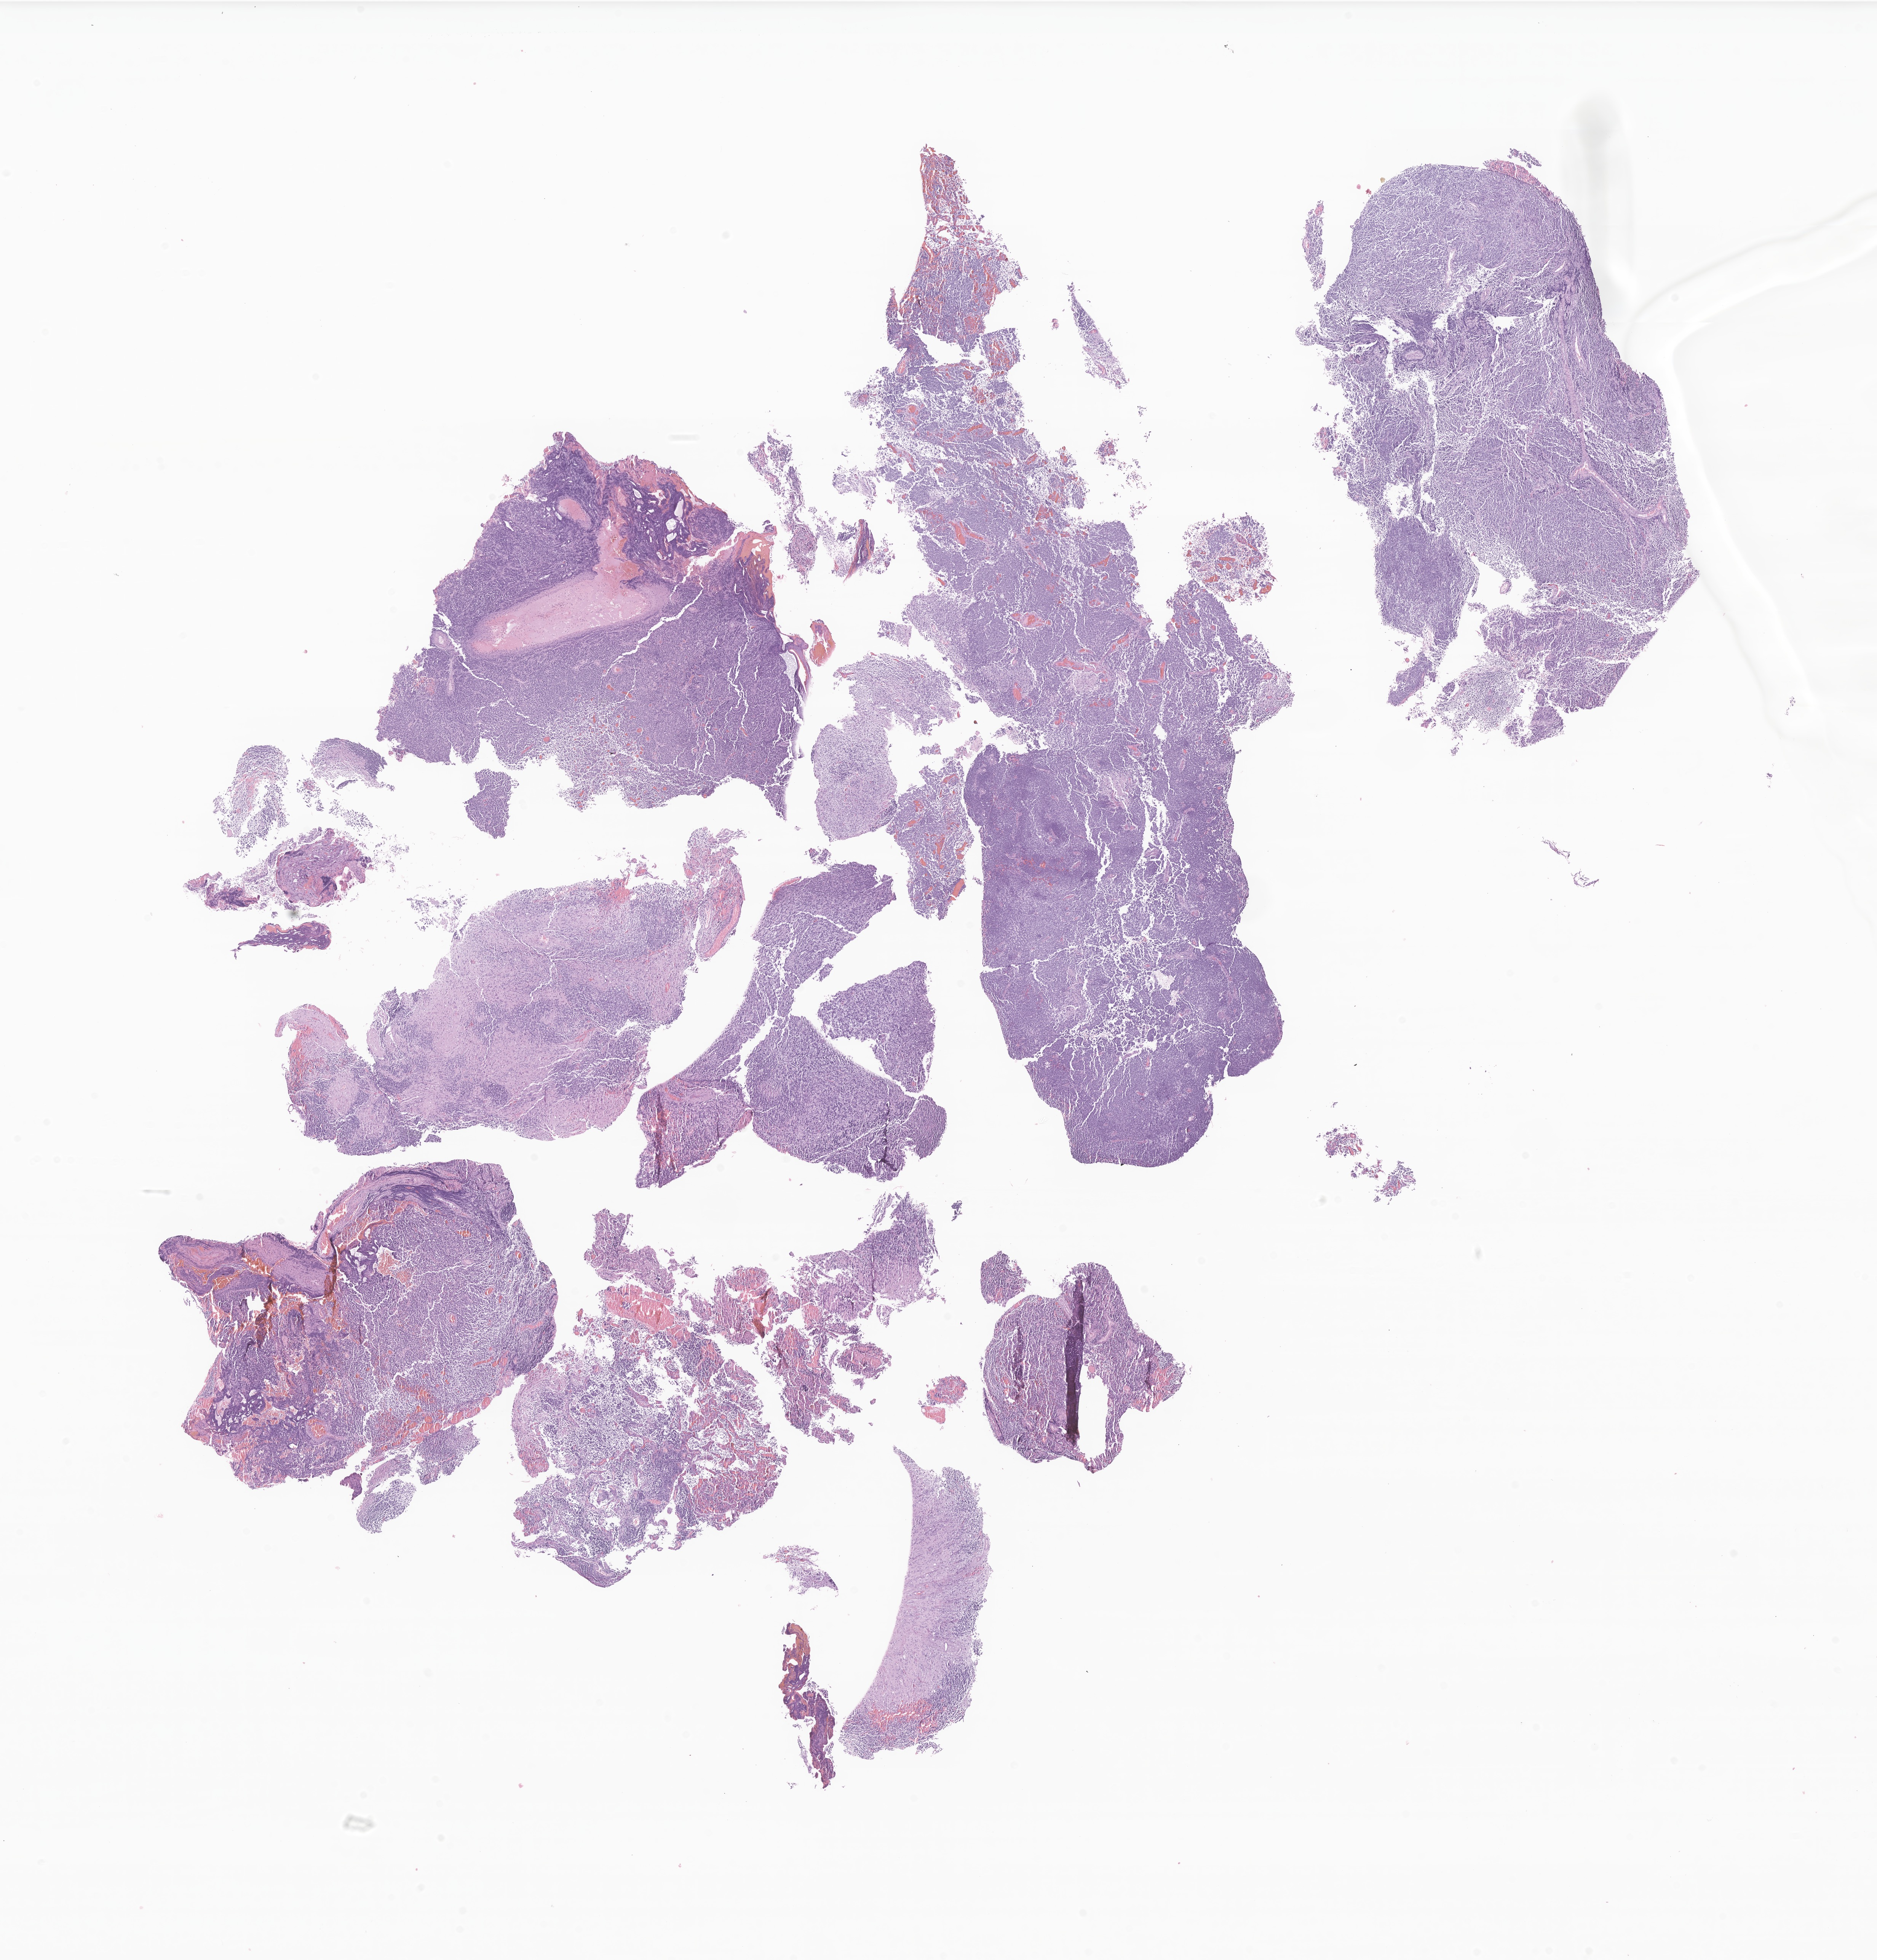
H&E whole-slide image of tumor tissue from the brain, a low-resolution overview of the entire scanned area, about 20.8 x 21.7 mm; FFPE section. Female patient, age 94 months (7 years 10 months).
Diagnosis: Medulloblastoma, NOS.